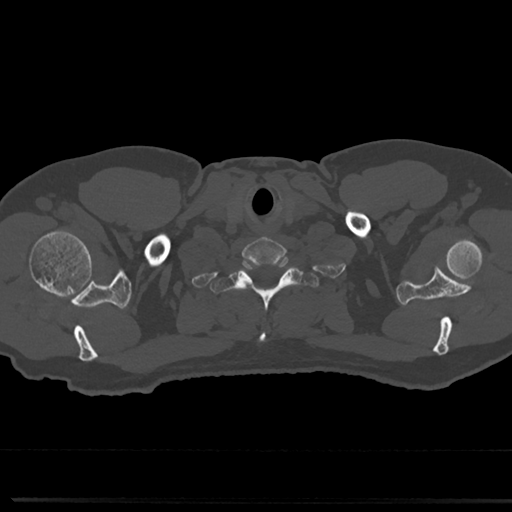
CT including the spine, one axial slice. Slice 684 of 817 in the series (ordered by position). Reconstruction kernel Br40s/3. 120 kVp. Bone window (W 1800 / L 400 HU). 0.5 mm slice thickness. 512 × 512 image matrix, field of view 355 × 355 mm. Patient: male, 61 years. Case-level facts recorded for this patient, not image findings: primary cancer: prostate.
Structures marked on this image (semi-automatically segmented with operator editing):
- T1 vertebra: bounding box [x1, y1, x2, y2] px = [217, 258, 315, 345]